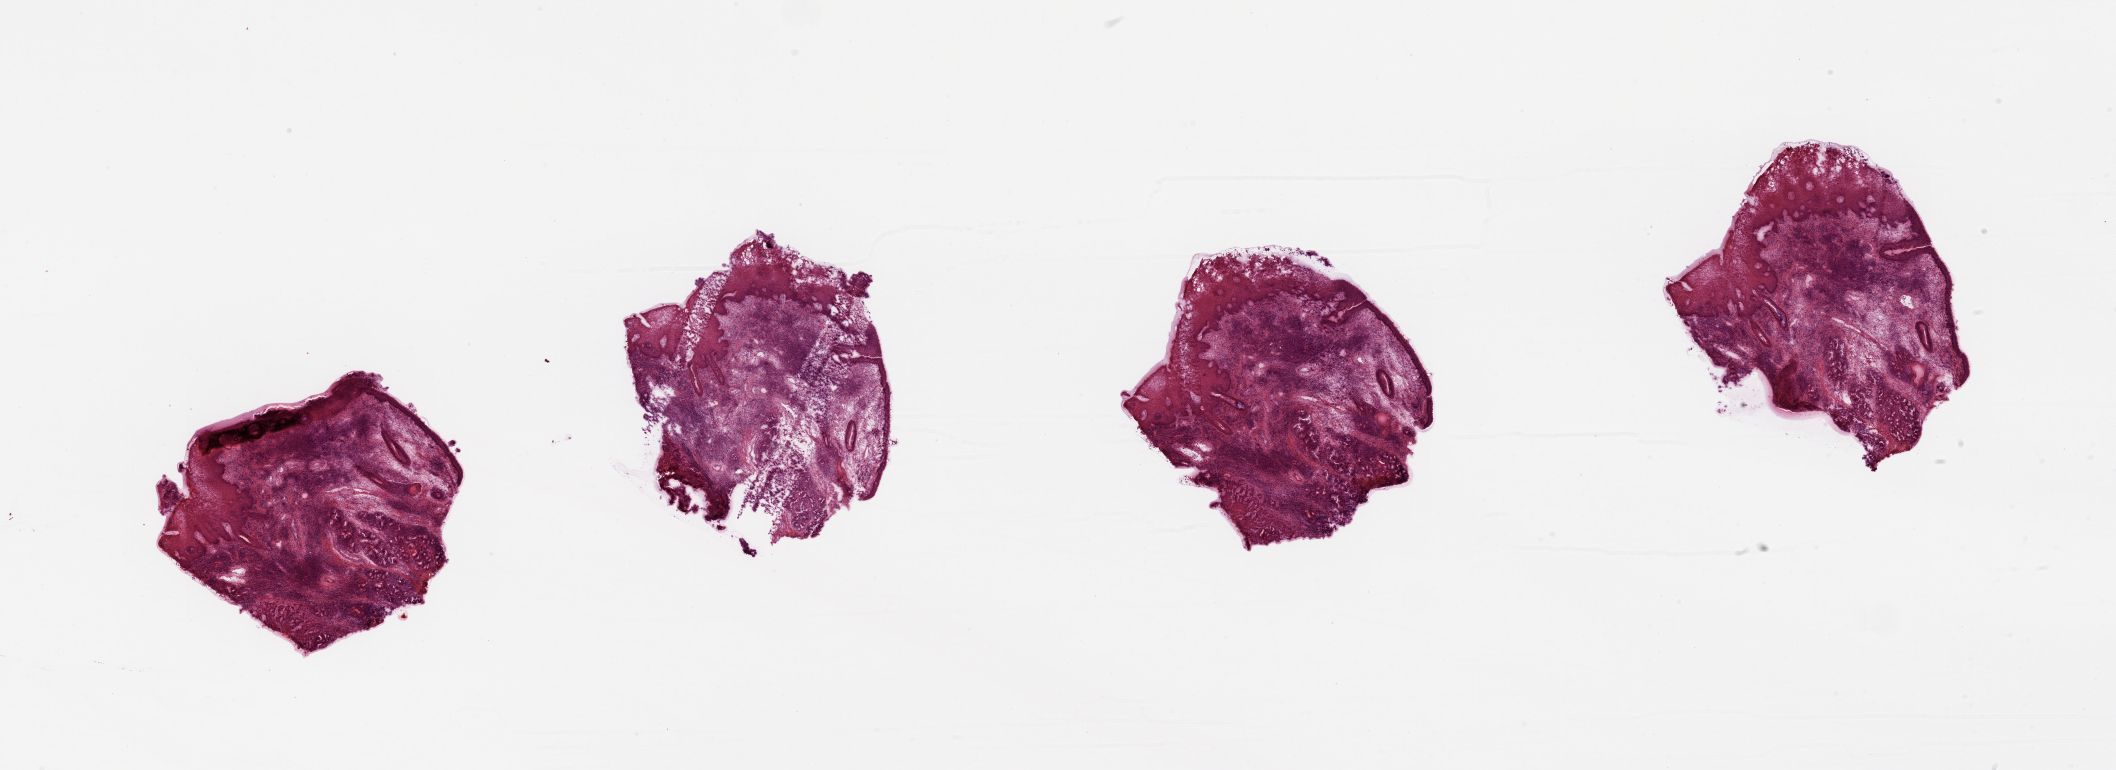
Digitized H&E tissue section (whole slide) — shown as a low-resolution overview of the whole scanned area (about 33.5 x 12.2 mm, from a 20x scan); tumour tissue sample, sampled site: larynx. 54-year-old female patient. Histologic grade: G2 (moderately differentiated). Slide review estimates, as recorded: tumour nuclei 40%, necrosis 5%.
• AJCC pathologic stage: III
• histologic diagnosis: Squamous cell carcinoma, NOS (larynx, NOS)